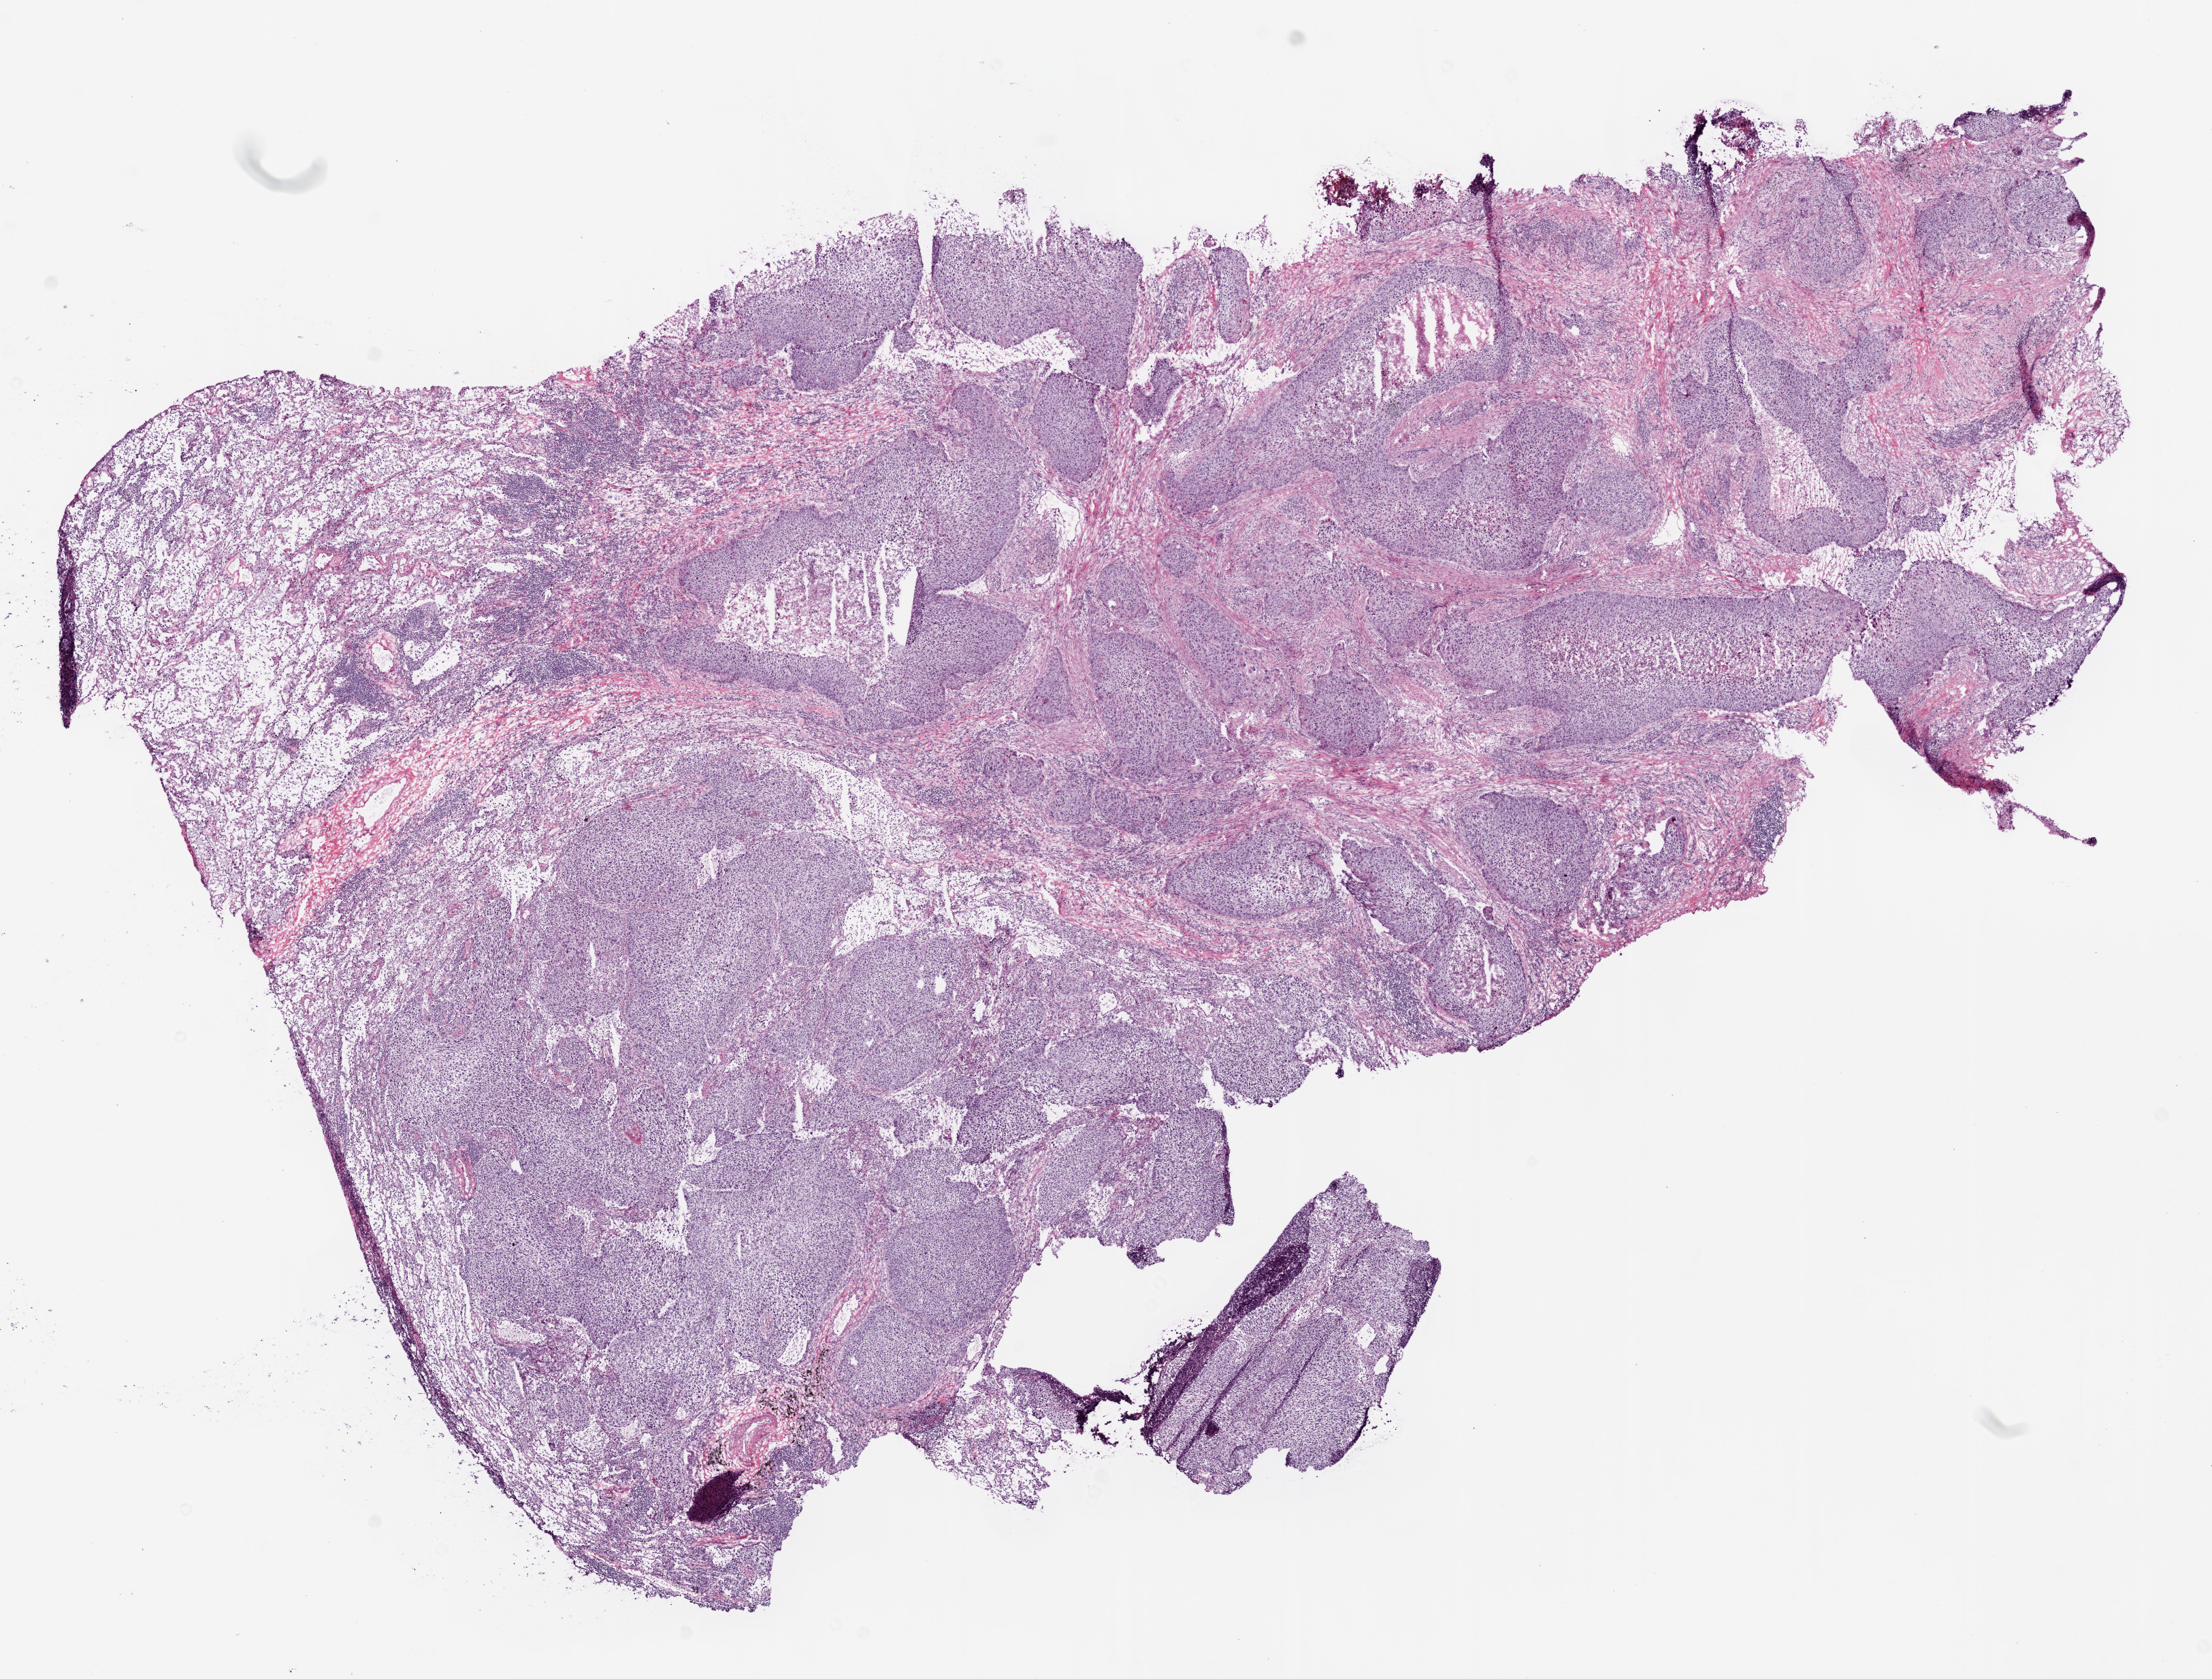
H&E whole-slide image — whole scanned area (about 13.0 x 9.9 mm, slide scanned at 20x) shown as a low-resolution overview. Frozen section from the bottom of the tissue portion. Primary tumour sample from the lung. Patient: male, age at initial diagnosis 70 years. Pathologist review of this section (percent, as recorded): tumour cells 70%, tumour nuclei 90%, normal cells 0%, stromal cells 25%, necrosis 5%. Infiltration values recorded for this section: lymphocyte infiltration 5%.
- laterality: right
- TNM: T2 N1 M1
- AJCC pathologic stage: IV (5th edition)
- pathologic diagnosis: Squamous cell carcinoma, NOS (upper lobe, lung)